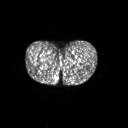
FDG PET of an extremity soft-tissue mass (from a PET/CT study), one axial slice; slice 14 of 267 in the series (ordered by position); 3.27 mm slice thickness; 128 × 128 image matrix. Female patient, age 17 years. Case-level facts recorded for this patient, not image findings: histological type: epithelioid sarcoma; grade: intermediate; site of the primary tumour: right buttock.
Outlined on this slice (expert contour drawn on MRI and transferred to this co-registered scan by the dataset authors):
- gross tumour volume including surrounding oedema: box from (x=52, y=77) to (x=58, y=85) px